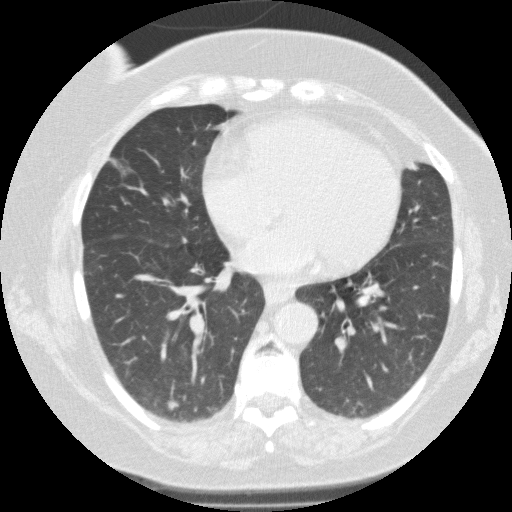
Low-dose screening chest CT, one axial slice. Position 61 of 146 along the scan axis. Reconstruction kernel FC01. 120 kVp. Lung window (W 1500 / L -600 HU). 512 × 512 image matrix.
Structures marked on this image (outlined manually by an expert reader):
- lesion 1 (nodule, lower lobe of right lung): bounding box <167,400,179,410> (left, top, right, bottom; pixels)